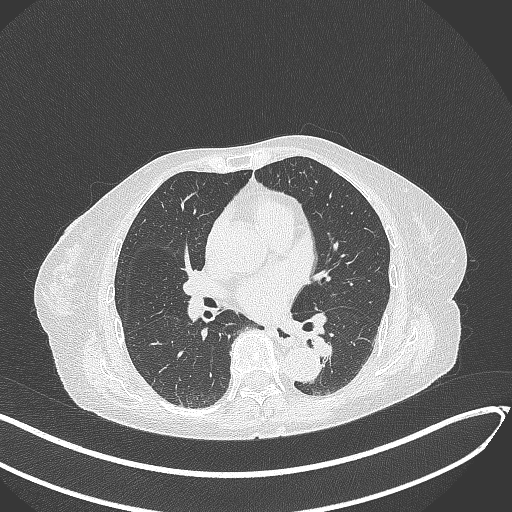
Chest CT, one axial slice. Position 127 of 324 along the scan axis. Reconstruction kernel B70f. Lung window (W 1500 / L -600 HU). 512 × 512 image matrix, field of view 400 × 400 mm. Female patient, age 82 years. From the clinical record (not read from this slice): clinical TNM (as recorded): T1b N0 M1.
Annotated regions visible in this slice (bounding box drawn by a radiologist):
- lung tumour (recorded histology: adenocarcinoma): box from (x=308, y=330) to (x=341, y=360) px